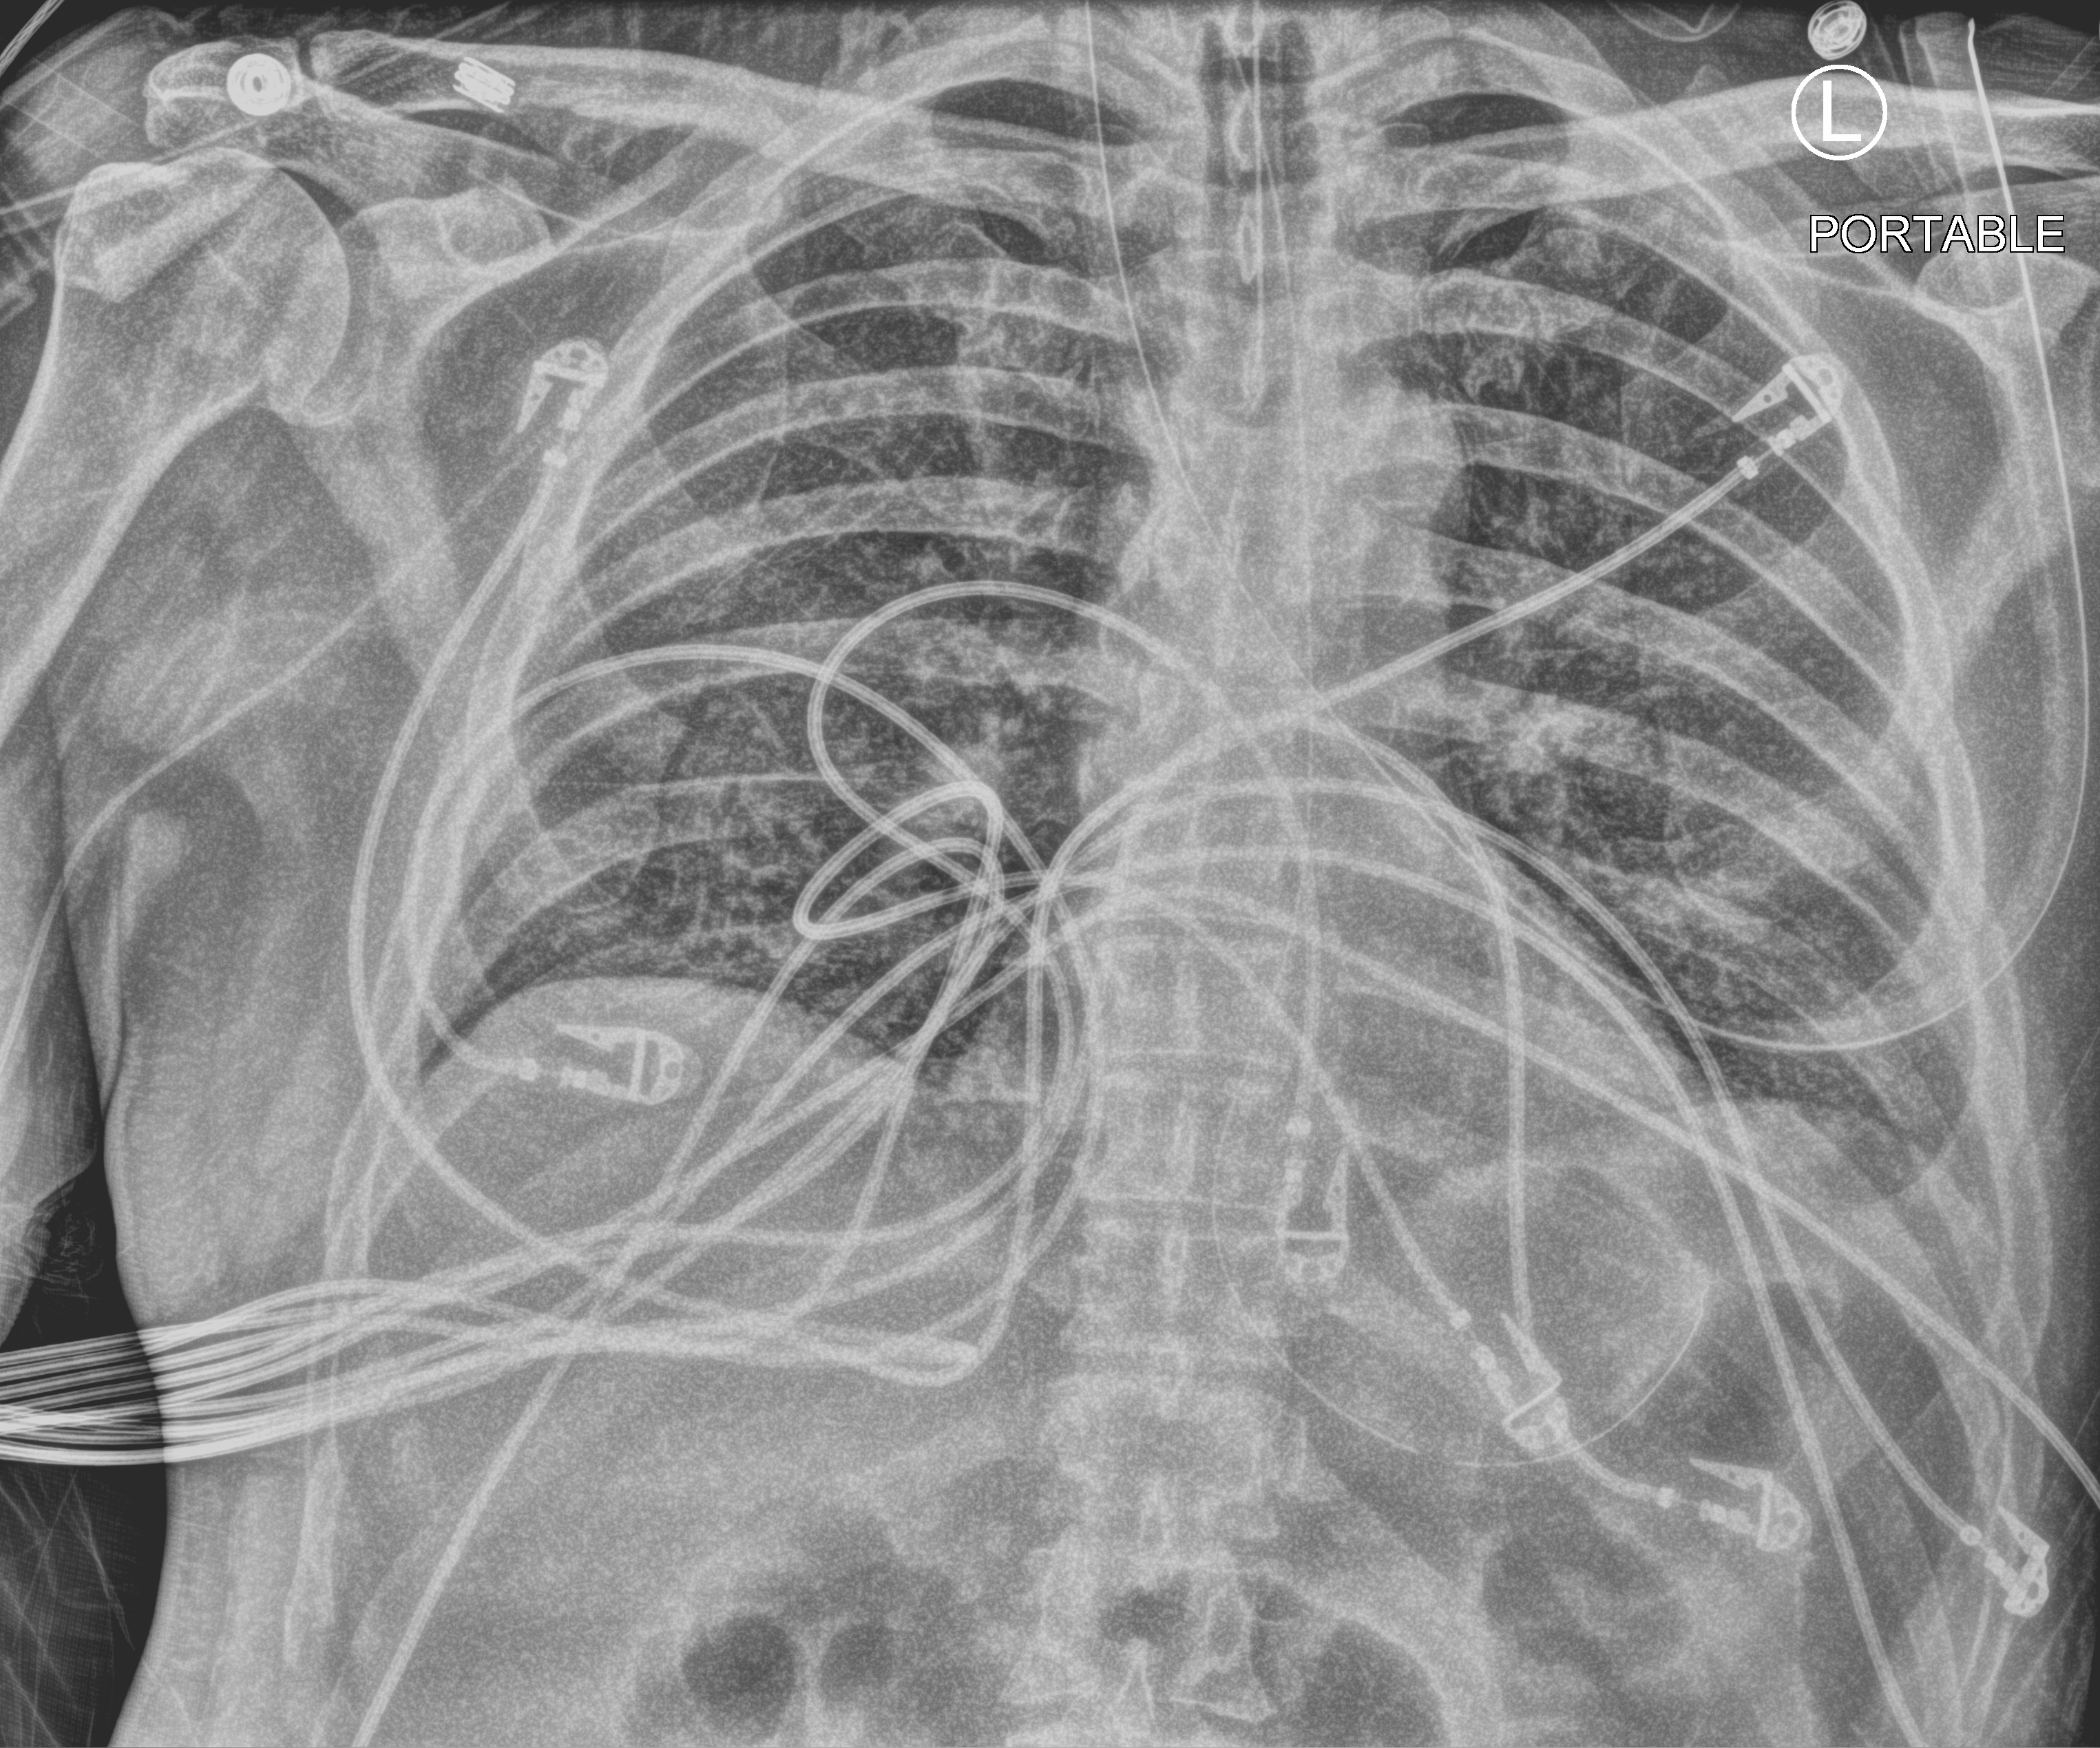
Bedside chest radiograph (computed radiography); anteroposterior (AP) projection. Male patient hospitalised with COVID-19, age 60–74 years.
From the hospital-stay record, not from the radiograph (when in the stay this image was taken is not recorded): mechanically ventilated during this hospital stay: yes.